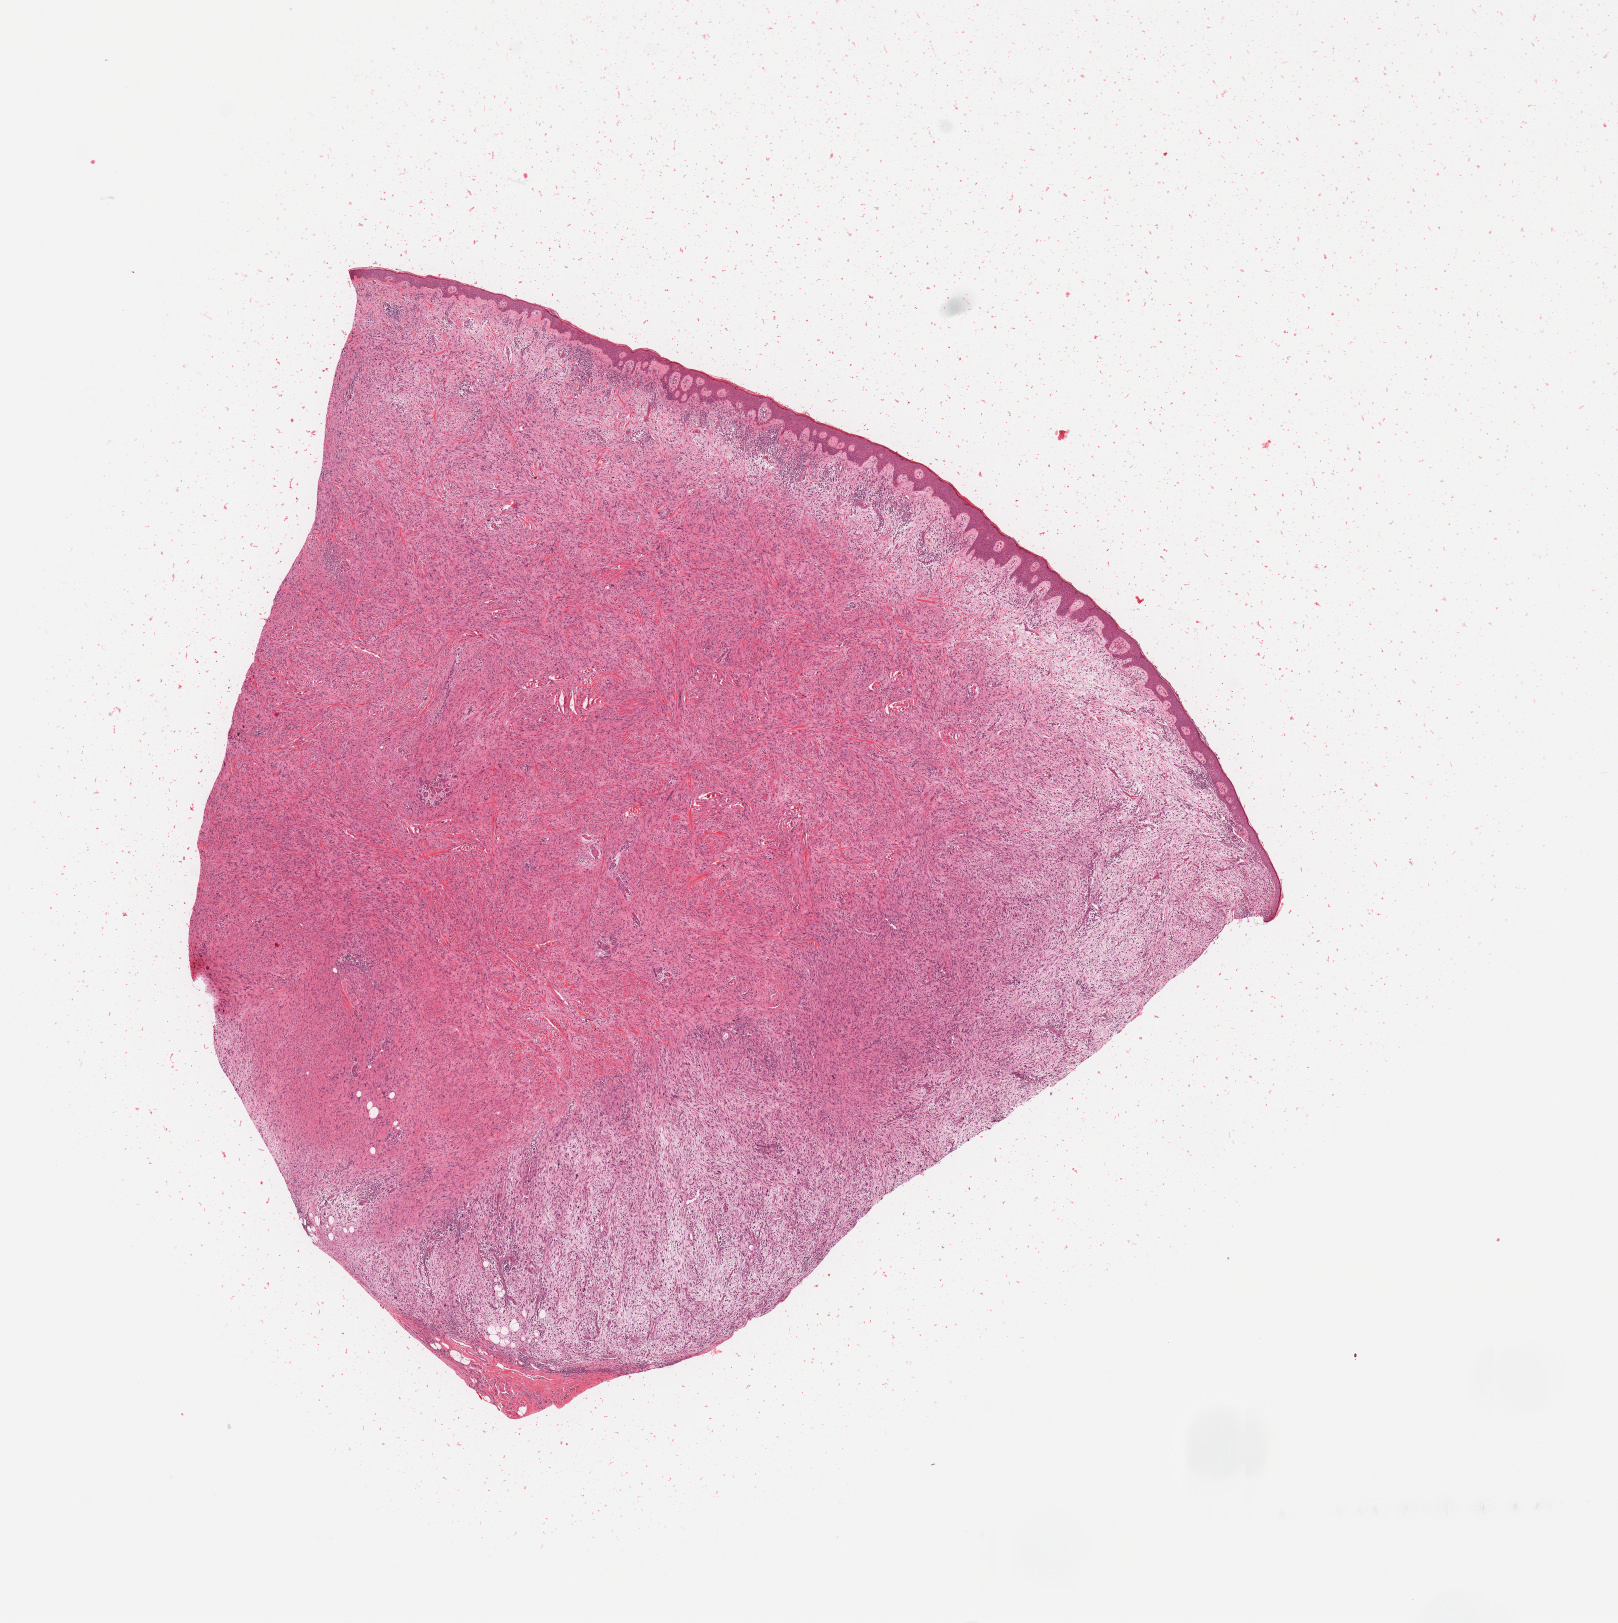
Digitized H&E tissue section (whole slide), whole scanned area (about 12.8 x 12.8 mm, slide scanned at 20x) shown as a low-resolution overview. Tumour tissue sample. Patient sex: female.
* patient diagnosis (cohort enrolment): sarcoma (site not recorded at cohort level)
* primary tumour site (as recorded): upper extremity